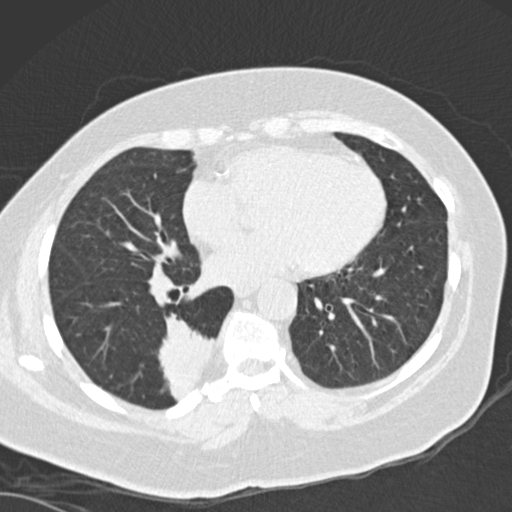
Low-dose screening chest CT, one axial slice; slice 66 of 162 in the series (ordered by position); reconstruction kernel B30f; 120 kVp; lung window (W 1500 / L -600 HU); 2 mm slice thickness; 512 × 512 image matrix, field of view 328 × 328 mm.
Structures marked on this image (outlined manually by an expert reader):
- lesion 1 (tumor, lower lobe of right lung): bounding box (x1, y1, x2, y2) in pixels: (158, 313, 216, 401)